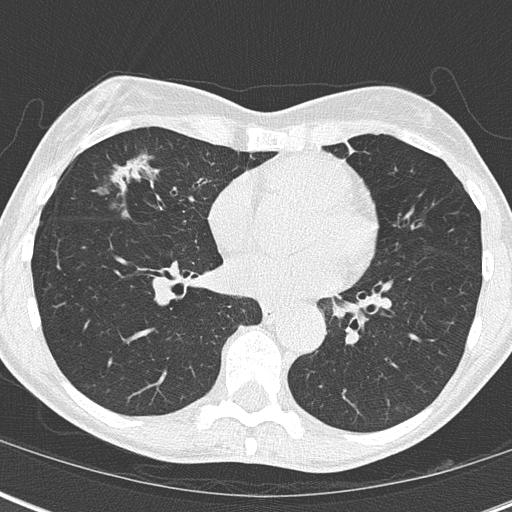
Low-dose screening chest CT, axial slice; third screening round (two years after baseline); lung window (W 1500 / L -600 HU); 2 mm slice thickness; lung (sharp) reconstruction kernel (B50f). Female participant, aged 67 years at enrolment. Current smoker at enrolment.
Lesion marked by an expert reader, bounding box <94,145,195,239> (left, top, right, bottom; pixels). The exam's reader record, not a measurement of the box and not confirmed to be the same lesion: non-calcified nodule or mass ≥4 mm, right middle lobe, 32 × 17 mm, mixed attenuation, pre-existing on the prior screen: yes; interval growth: yes. Lung cancer was diagnosed 76 days after this screen: bronchiolo-alveolar adenocarcinoma, NOS, right middle lobe, well differentiated (G1), stage IA (AJCC 6th edition), 25 mm at pathology.